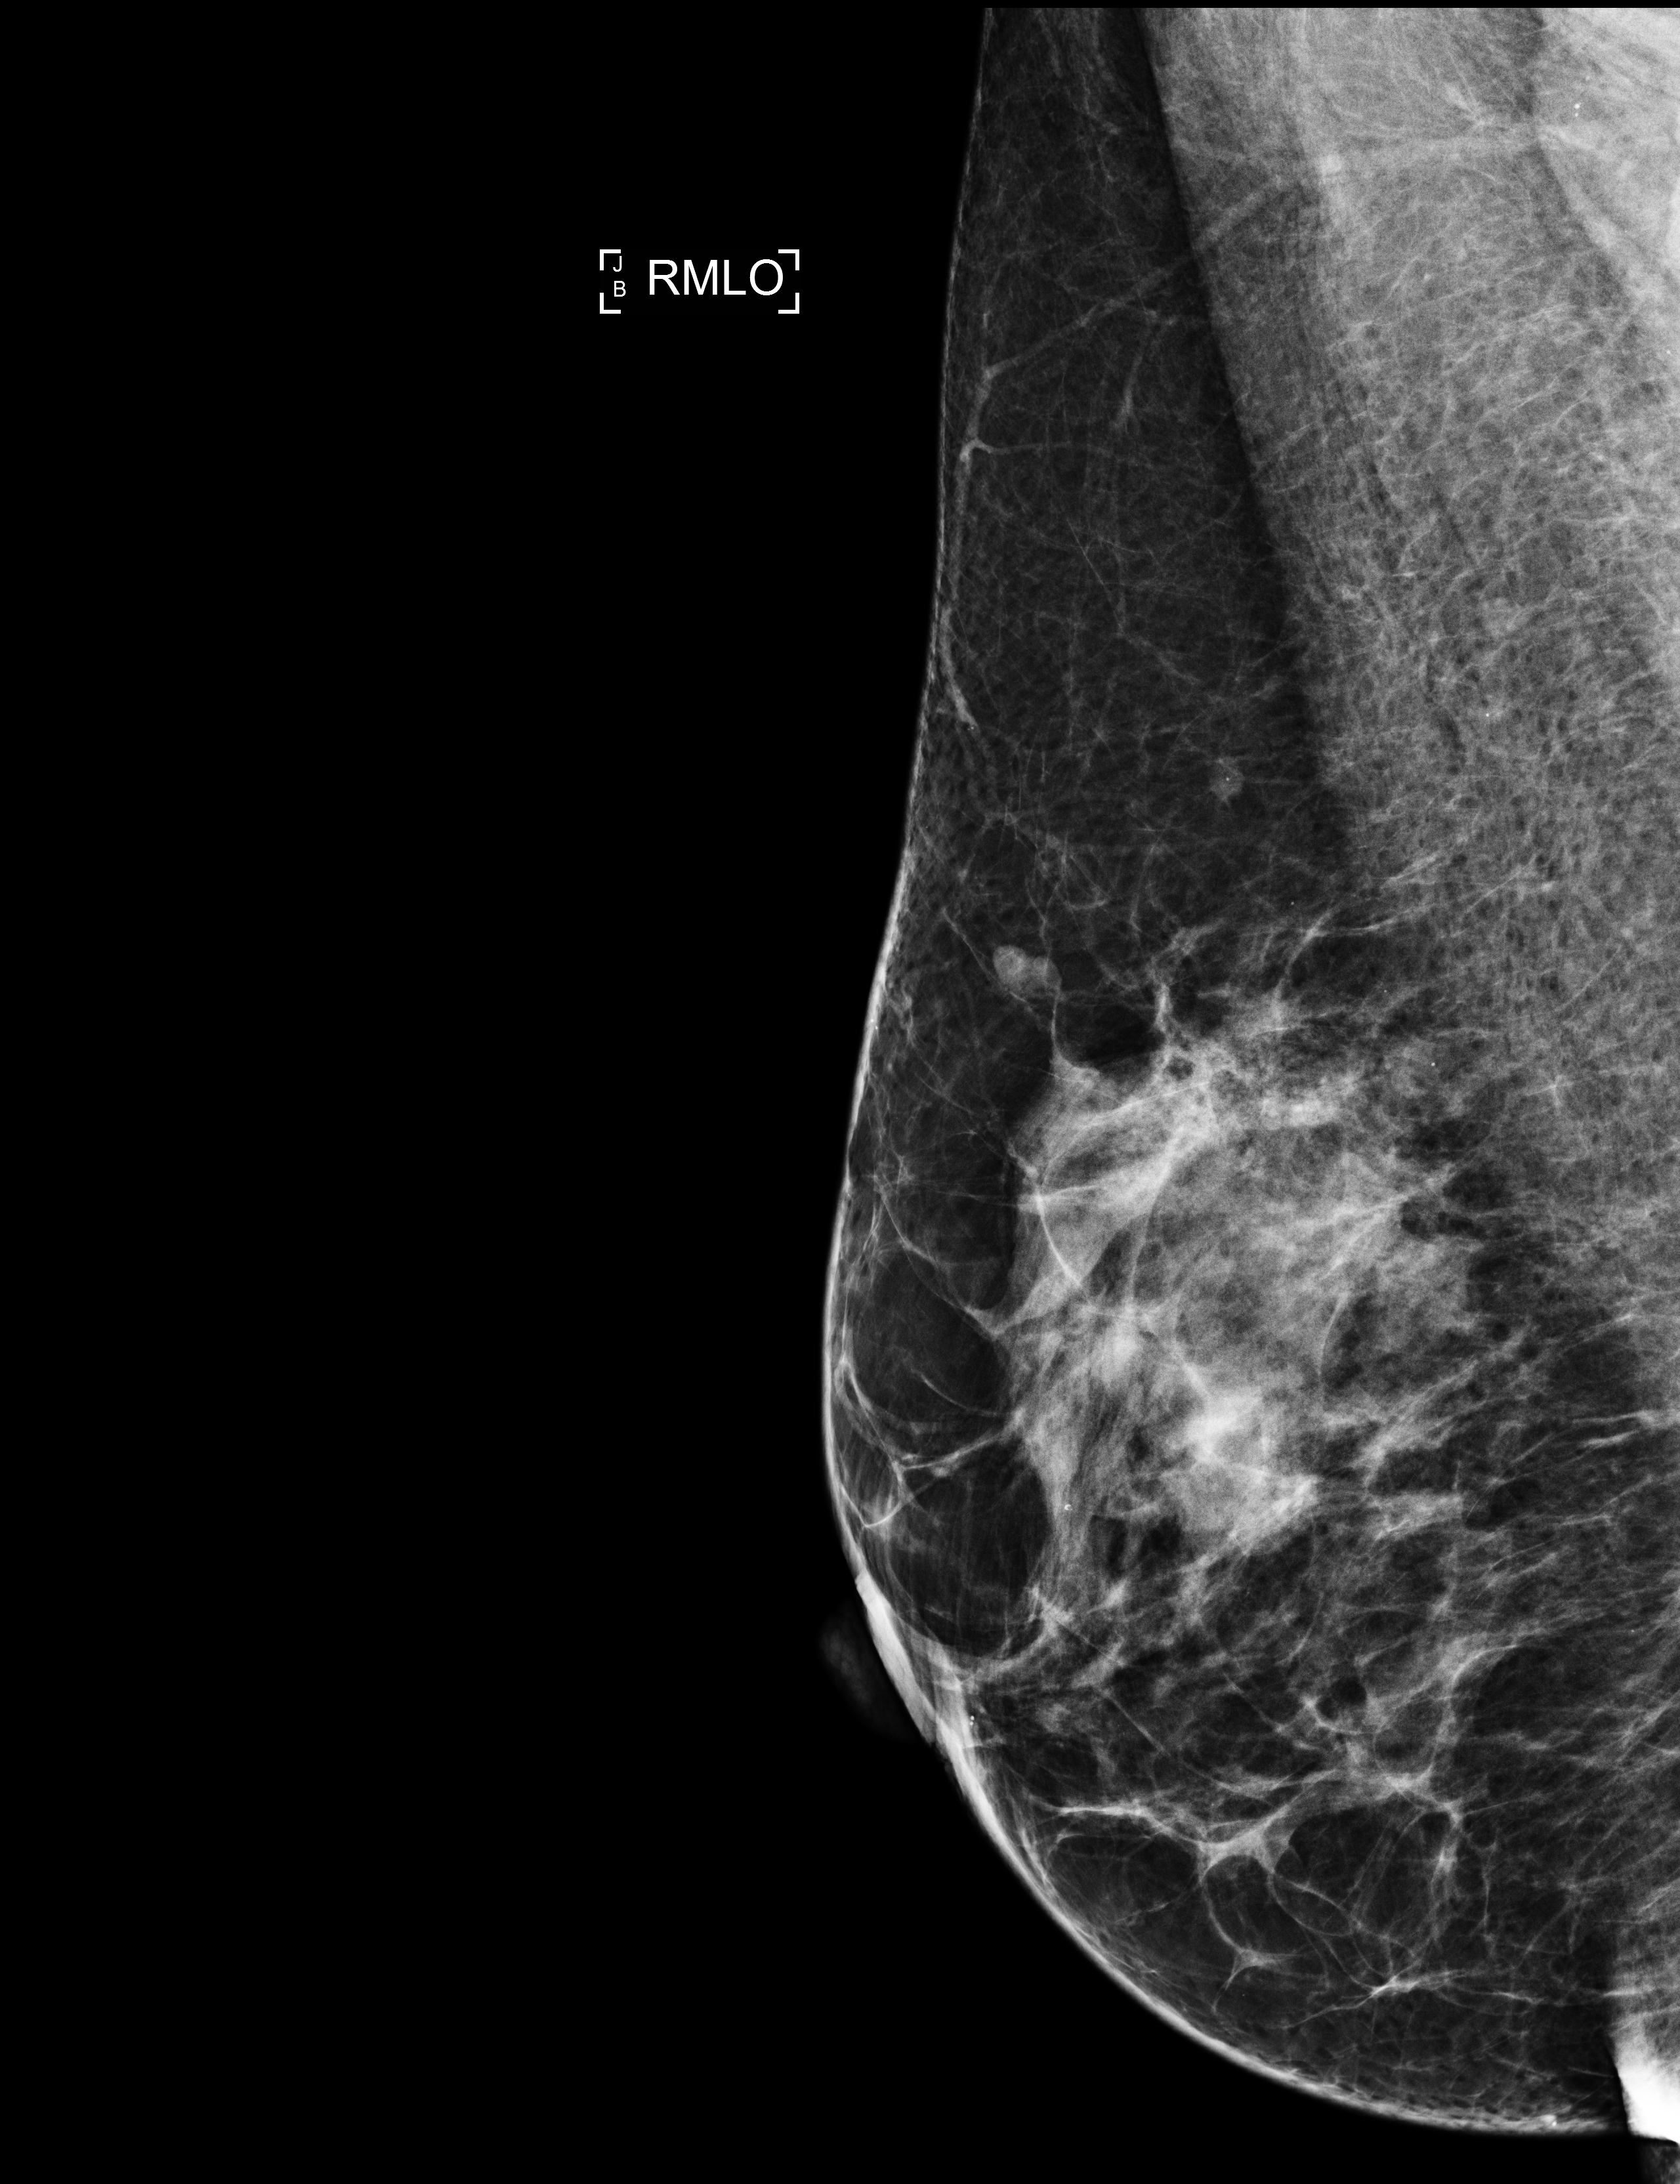
Annual screening mammography examination. Patient aged 61 years (female).
Image type: full-field digital mammogram. Breast: right. Projection: mediolateral oblique (MLO) view.